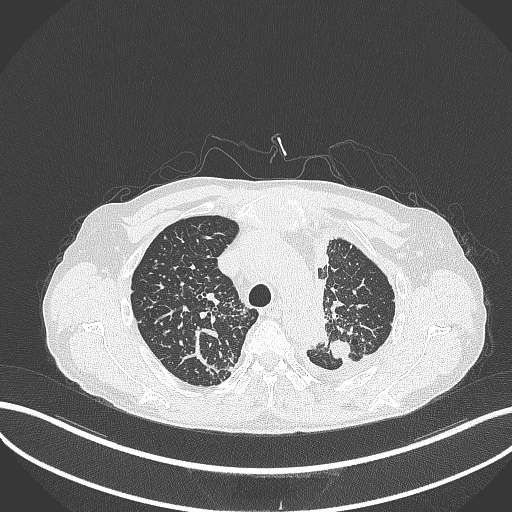
Chest CT, one axial slice. Reconstruction kernel B70f. 120 kVp. Lung window (W 1500 / L -600 HU). 1 mm slice thickness. 512 × 512 image matrix, field of view 400 × 400 mm. Patient: male, 58 years. Case-level facts recorded for this patient, not image findings: clinical TNM (as recorded): T1c N3 M1.
Outlined on this slice (bounding box drawn by a radiologist):
- lung tumour (recorded histology: adenocarcinoma): bounding box (x1, y1, x2, y2) in pixels: (328, 336, 351, 361)